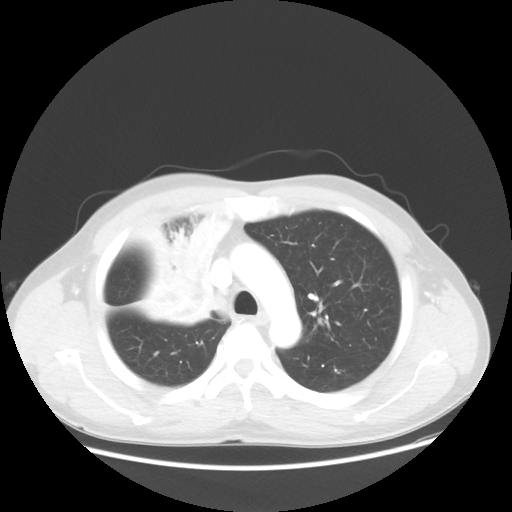
Chest CT, one axial slice. Lung window (W 1500 / L -600 HU). 5 mm slice thickness. 512 × 512 image matrix, field of view 398 × 398 mm. Male patient, age 60 years. Case-level facts recorded for this patient, not image findings: clinical TNM (as recorded): T2a N1 M0.
Outlined on this slice (rectangle marked by the reading radiologist):
- lung tumour (recorded histology: squamous cell carcinoma): box from (x=125, y=203) to (x=233, y=330) px